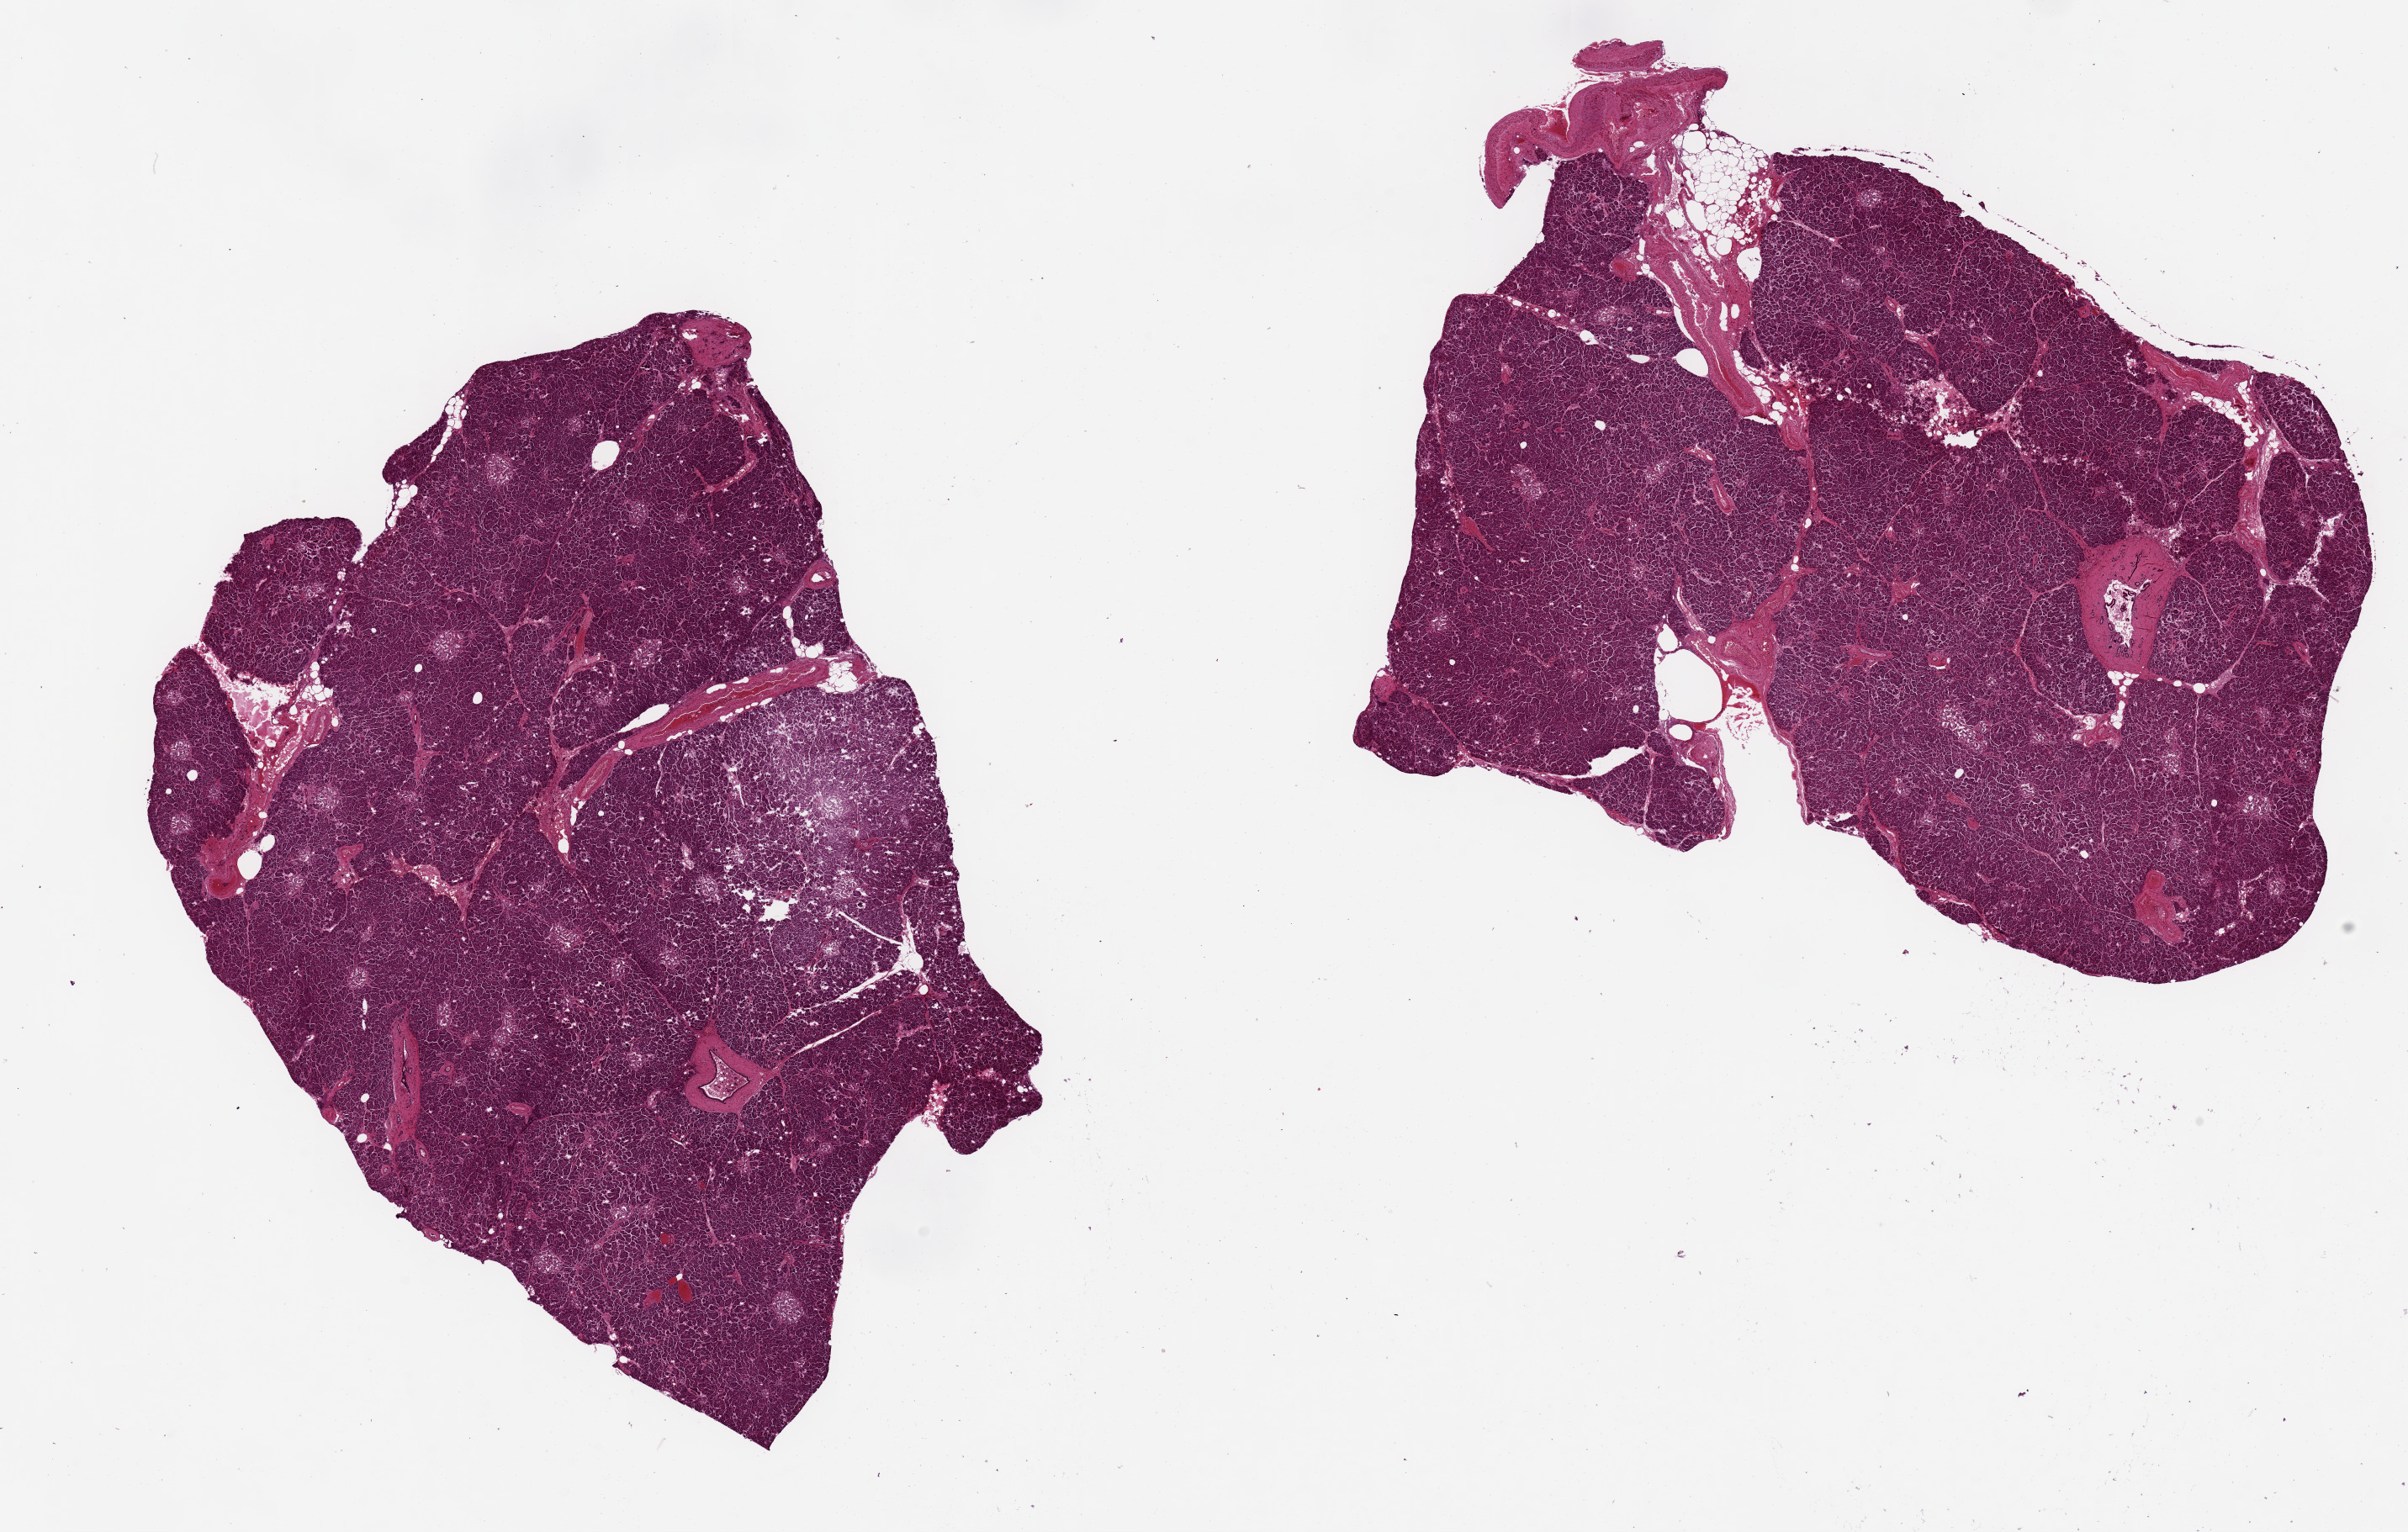
Haematoxylin and eosin whole-slide image, brightfield, whole scanned area (about 22.6 x 14.4 mm, slide scanned at 20x) shown as a low-resolution overview, PAXgene-fixed paraffin-embedded (PFPE) section, section of pancreas (target tissue), donor tissue sample. Female donor.
Review note (as recorded): 2 aliquots, ~10x7mm, minimal interstitial fat, peripheral saponifcation, moderate.